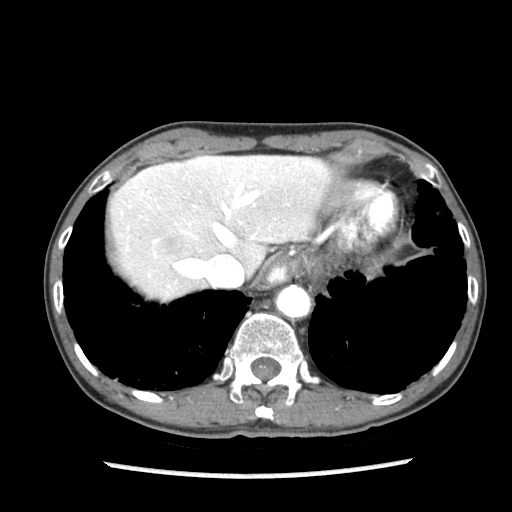
Contrast-enhanced abdominal CT (liver protocol), one axial slice. Slice 69 of 87 in the series (ordered by position). Reconstruction kernel STANDARD. Soft-tissue window (W 400 / L 40 HU). 2.5 mm slice thickness. 512 × 512 image matrix. Case-level facts recorded for this patient, not image findings: diagnosis: hepatocellular carcinoma (patient treated with transarterial chemoembolisation; whether this scan precedes or follows treatment is not stated here); TNM stage (as recorded): Stage-IIIB.
Structures marked on this image (semi-automatic segmentation, software-assisted and operator-edited):
- liver parenchyma outside the tumour (the mass and vessels are separate outlines, so this box may not span the whole liver): box from (x=110, y=154) to (x=332, y=300) px
- mass: (x=162, y=232)–(x=182, y=251)
- liver vessels: (x=154, y=164)–(x=297, y=278)